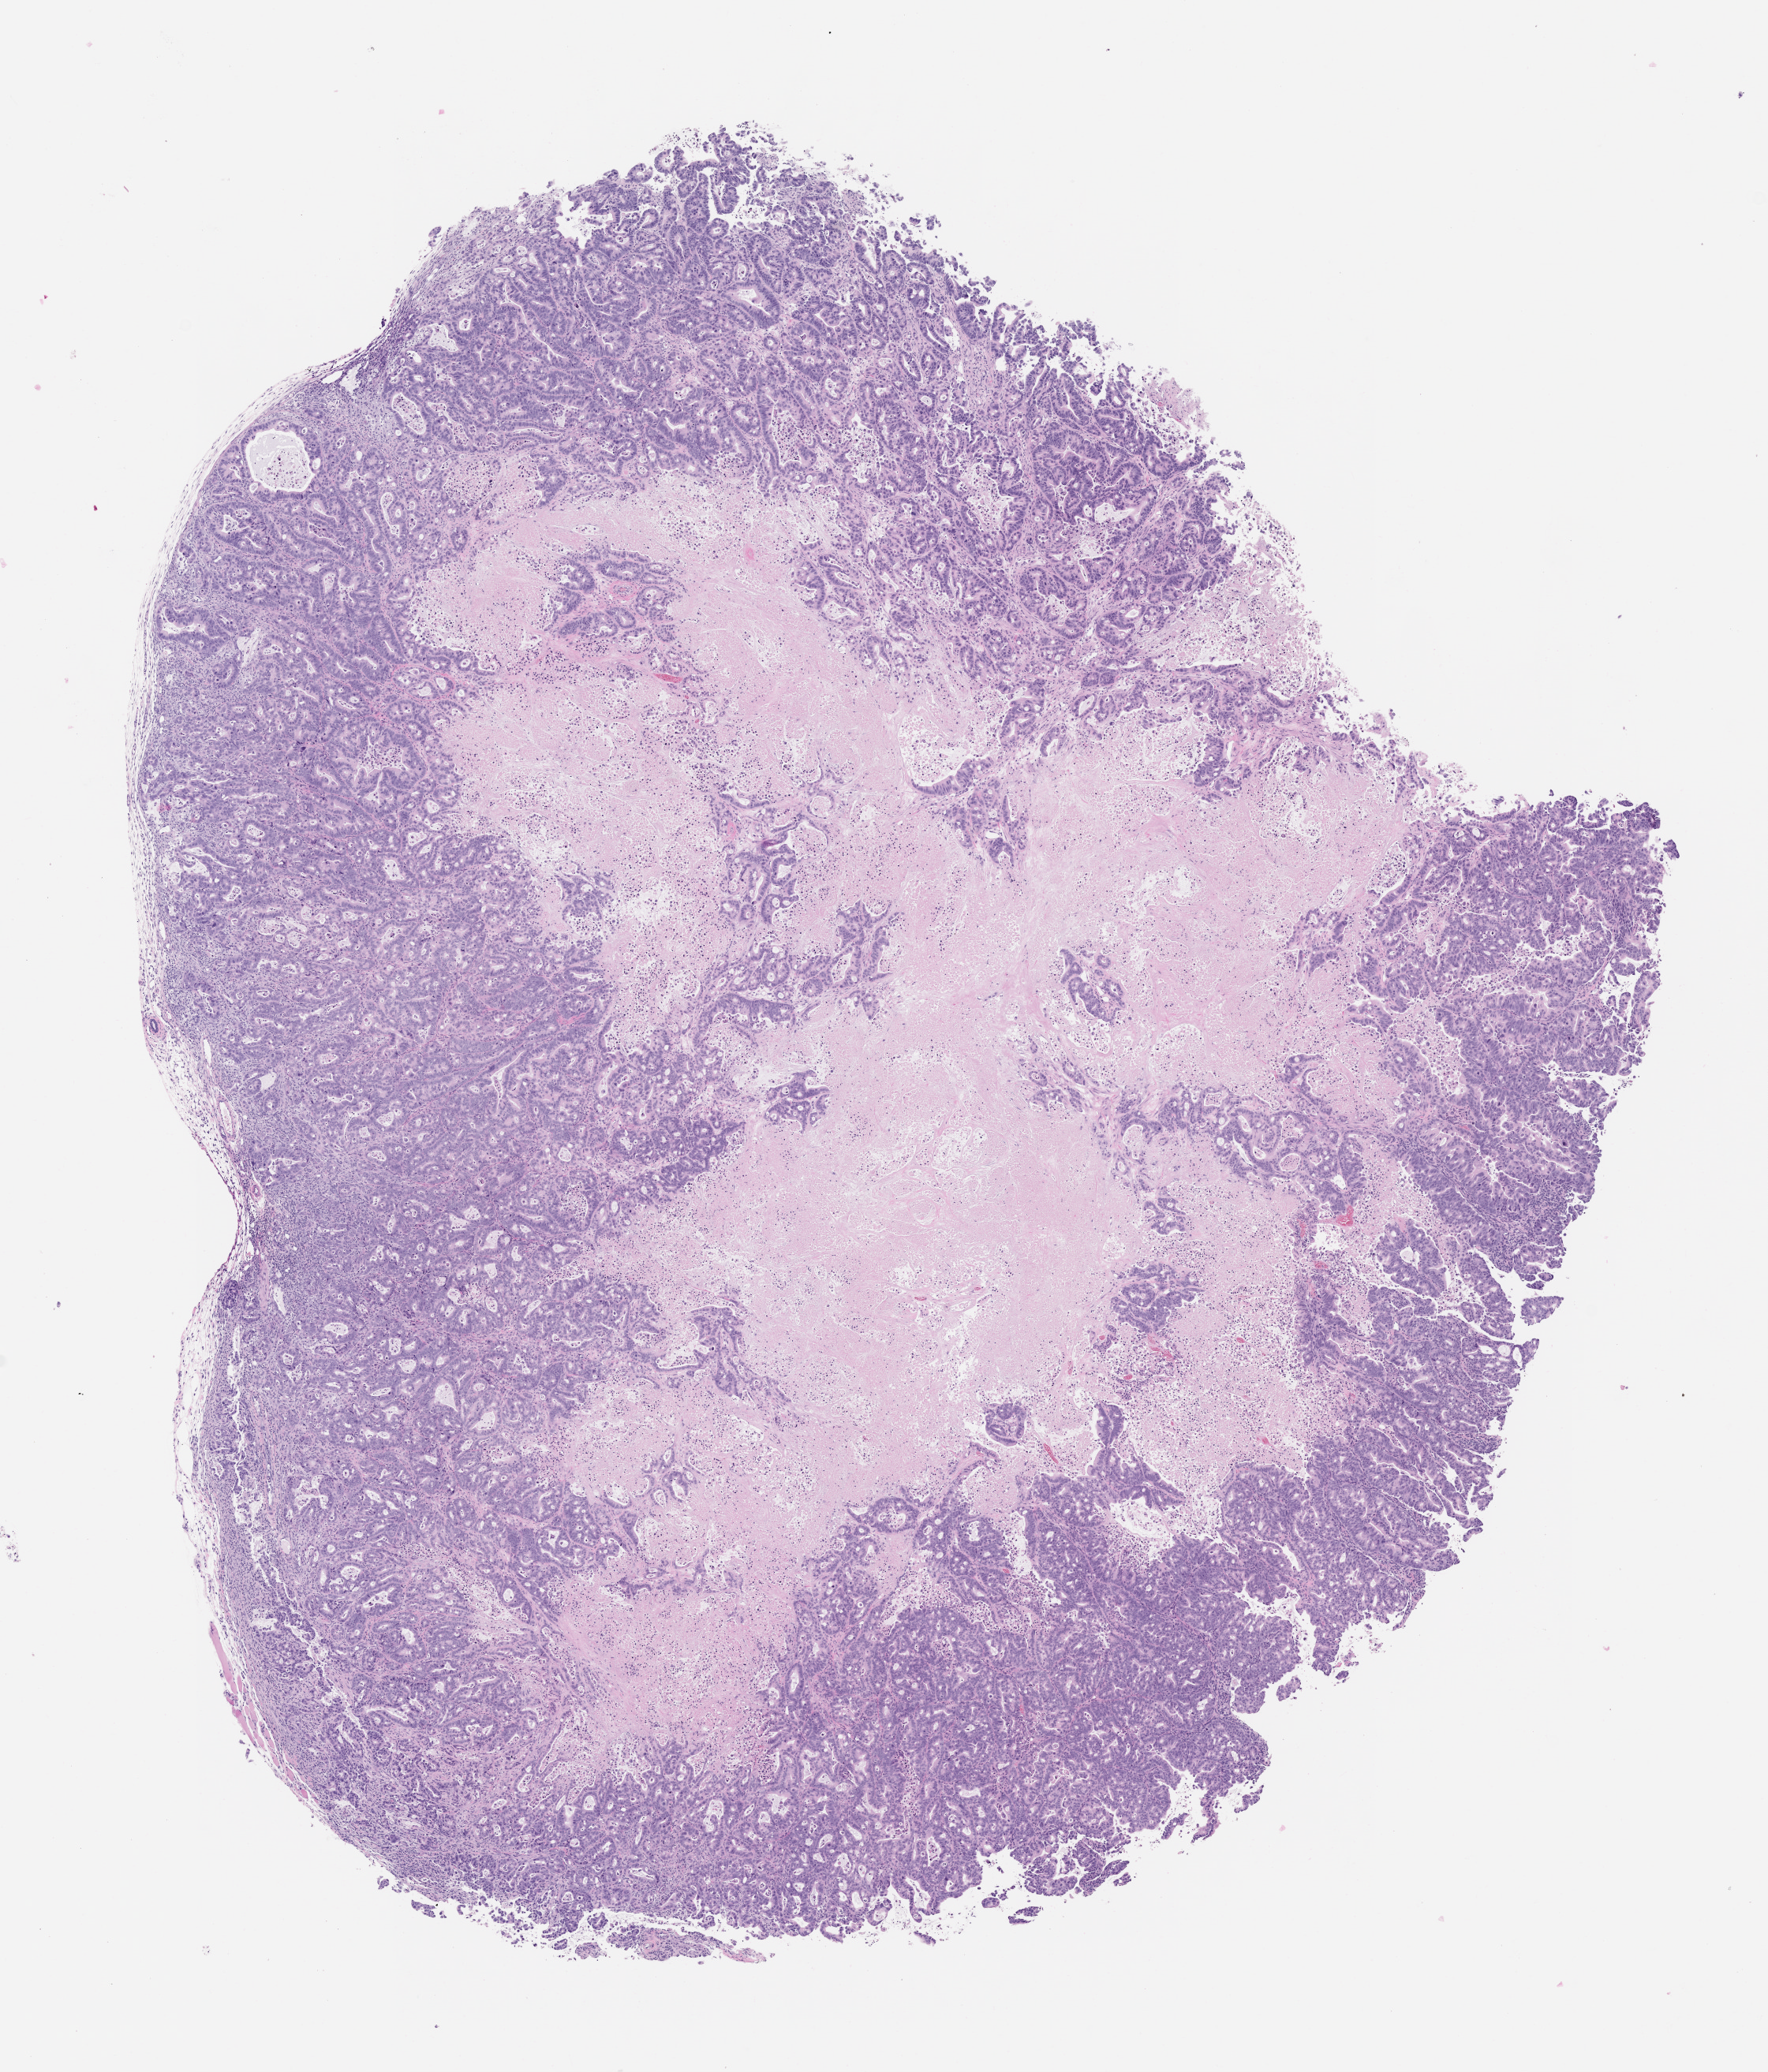
H&E whole-slide image of a patient-derived xenograft (PDX) tumor grown in a mouse, passage 4, shown as a low-resolution overview of the whole scanned area (about 9.0 x 10.6 mm), formalin-fixed paraffin-embedded section, tumor site category: pancreas.
- originating patient diagnosis: Pancreatic Adenocarcinoma